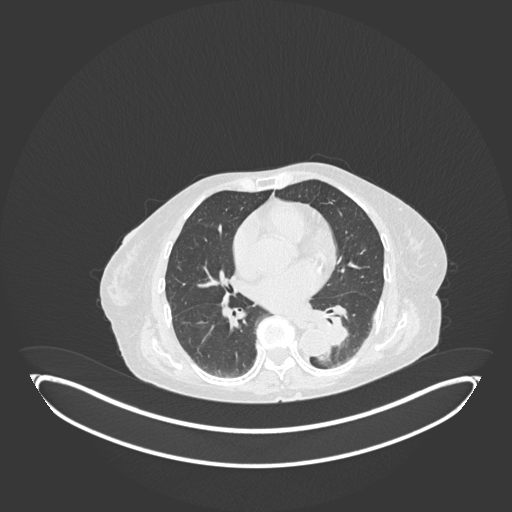
Chest CT, one axial slice; slice 53 of 189 in the series (ordered by position); reconstruction kernel B30f; 120 kVp; lung window (W 1500 / L -600 HU); 1 mm slice thickness; 512 × 512 image matrix. Female patient, age 82 years. From the clinical record (not read from this slice): clinical TNM (as recorded): T1b N0 M1.
Structures marked on this image (bounding box drawn by a radiologist):
- lung tumour (recorded histology: adenocarcinoma): bounding box [x1, y1, x2, y2] px = [317, 311, 355, 352]